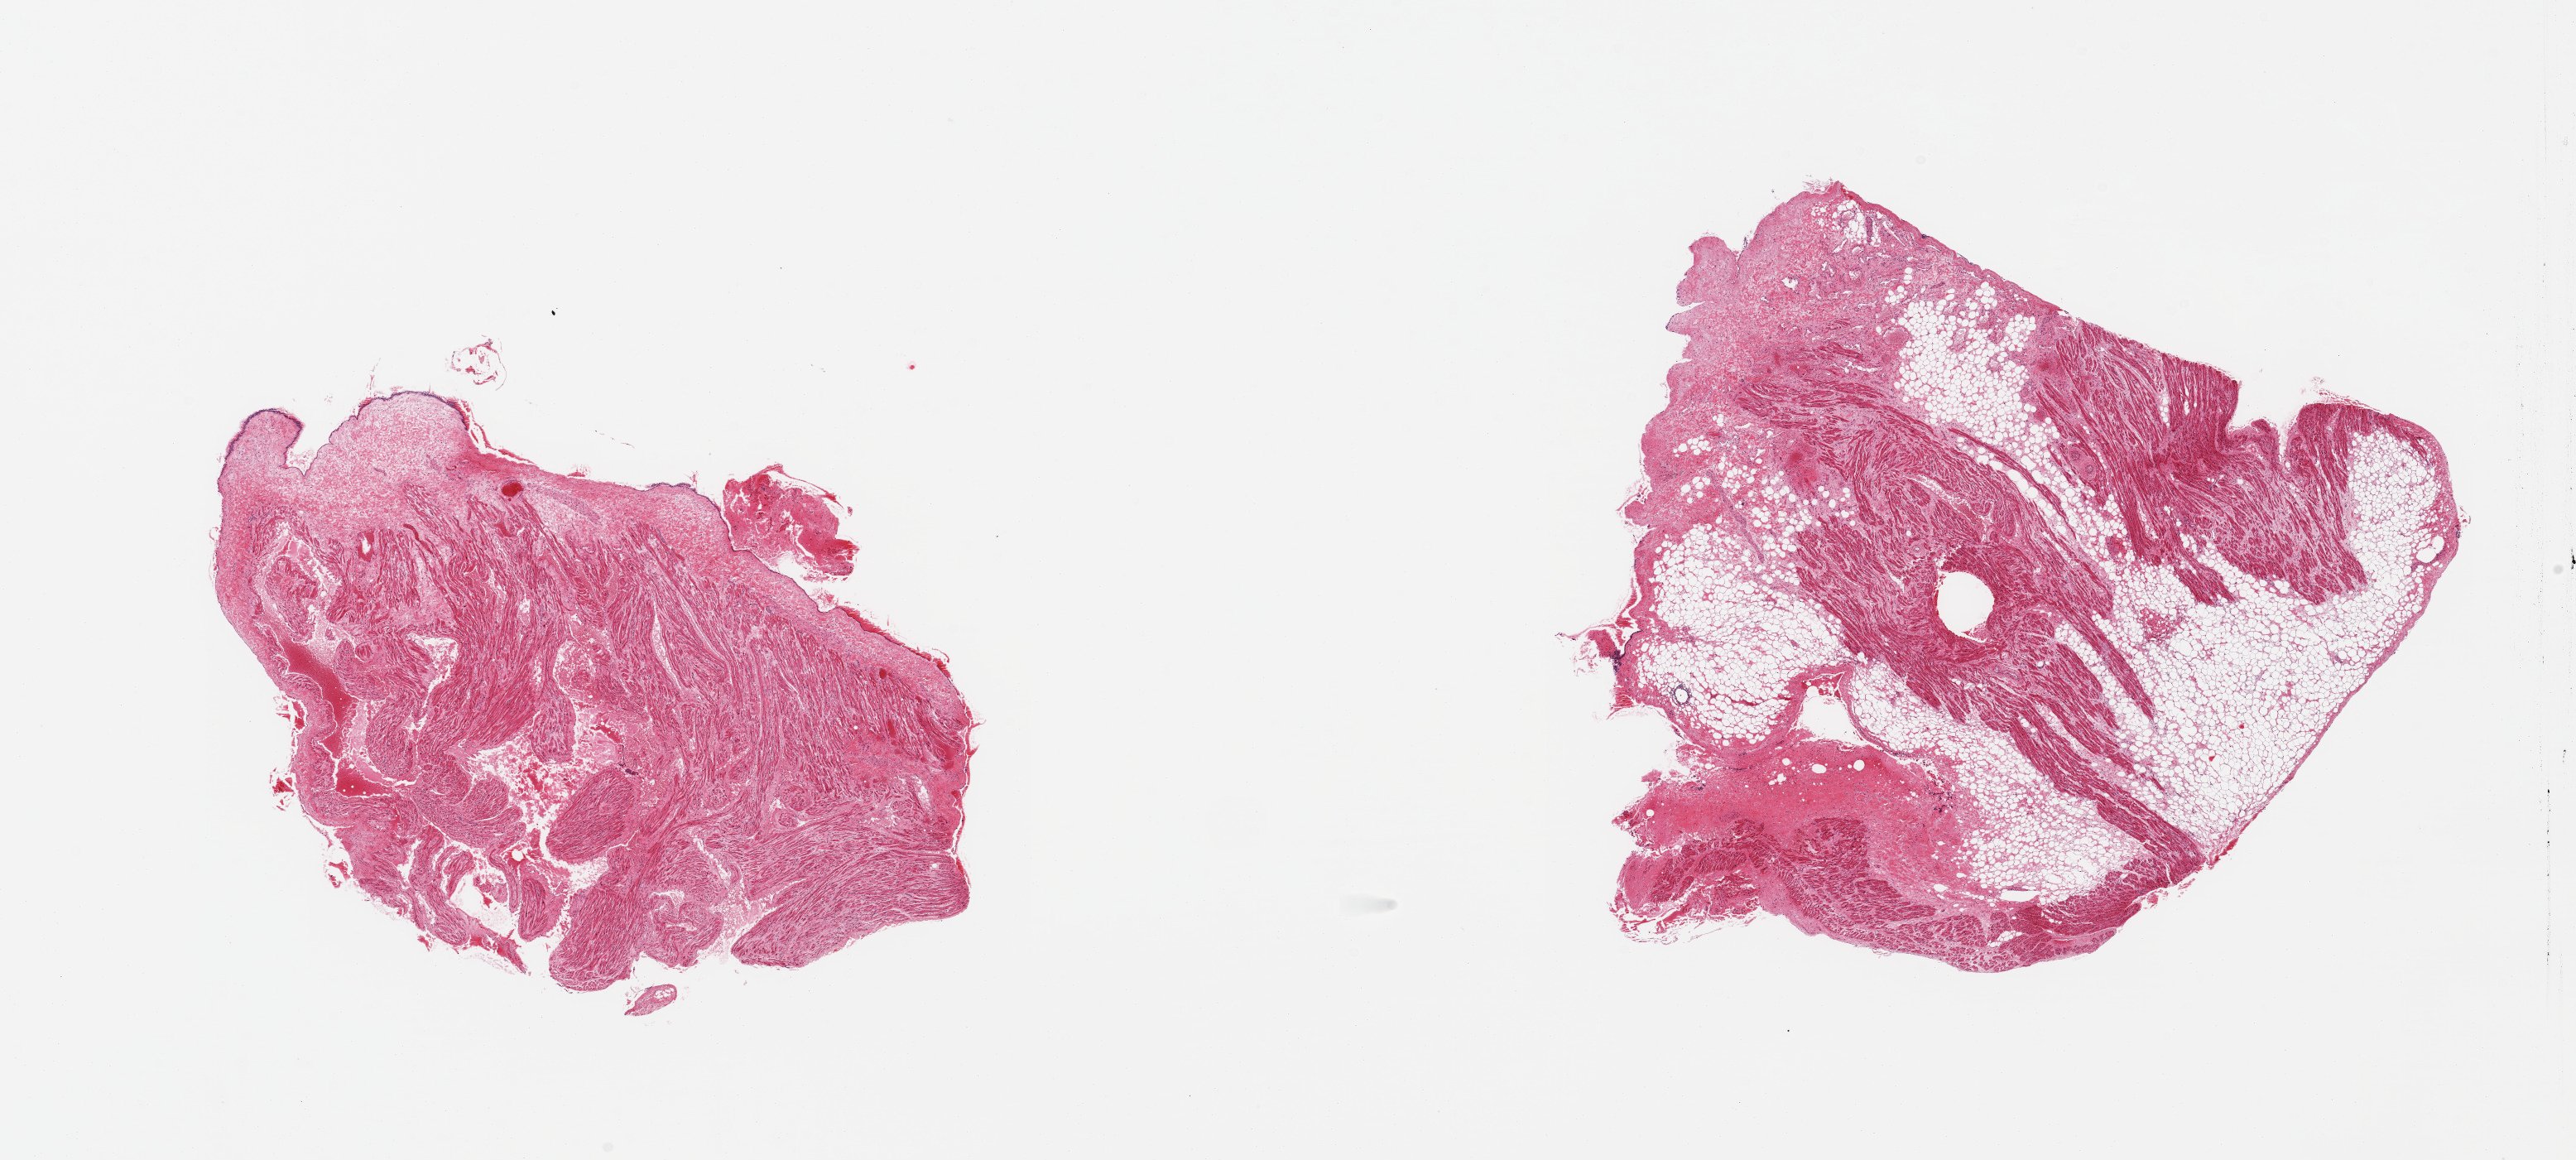
Haematoxylin and eosin whole-slide image — a low-resolution overview of the entire scanned area, about 24.6 x 11.1 mm (acquisition: 20x scan); PAXgene-fixed paraffin-embedded (PFPE) section; target tissue: auricular appendage; tissue donor sample. Donor sex: female.
• reviewer comment on this tissue sample: 2 pieces: 1 with 60% fatty and fibrous content